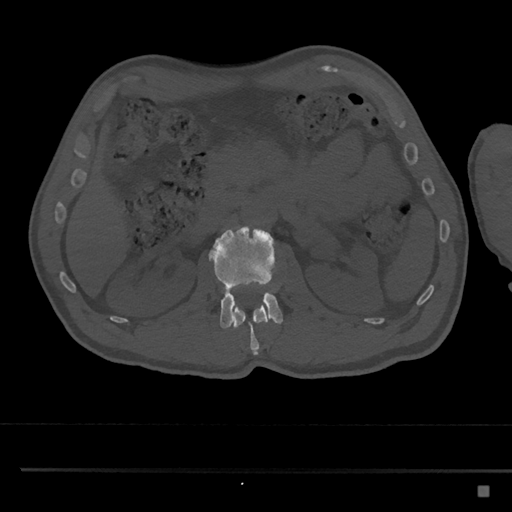
CT including the spine, one axial slice. Slice 789 of 797 in the series (ordered by position). 120 kVp. Bone window (W 1800 / L 400 HU). 0.5 mm slice thickness. 512 × 512 image matrix. Patient: male, 59 years. Case-level facts recorded for this patient, not image findings: primary cancer: prostate.
Annotated regions visible in this slice (semi-automatically segmented with operator editing):
- L1 vertebra: bounding box <233,300,269,355> (left, top, right, bottom; pixels)
- L2 vertebra: <208,226,283,329>